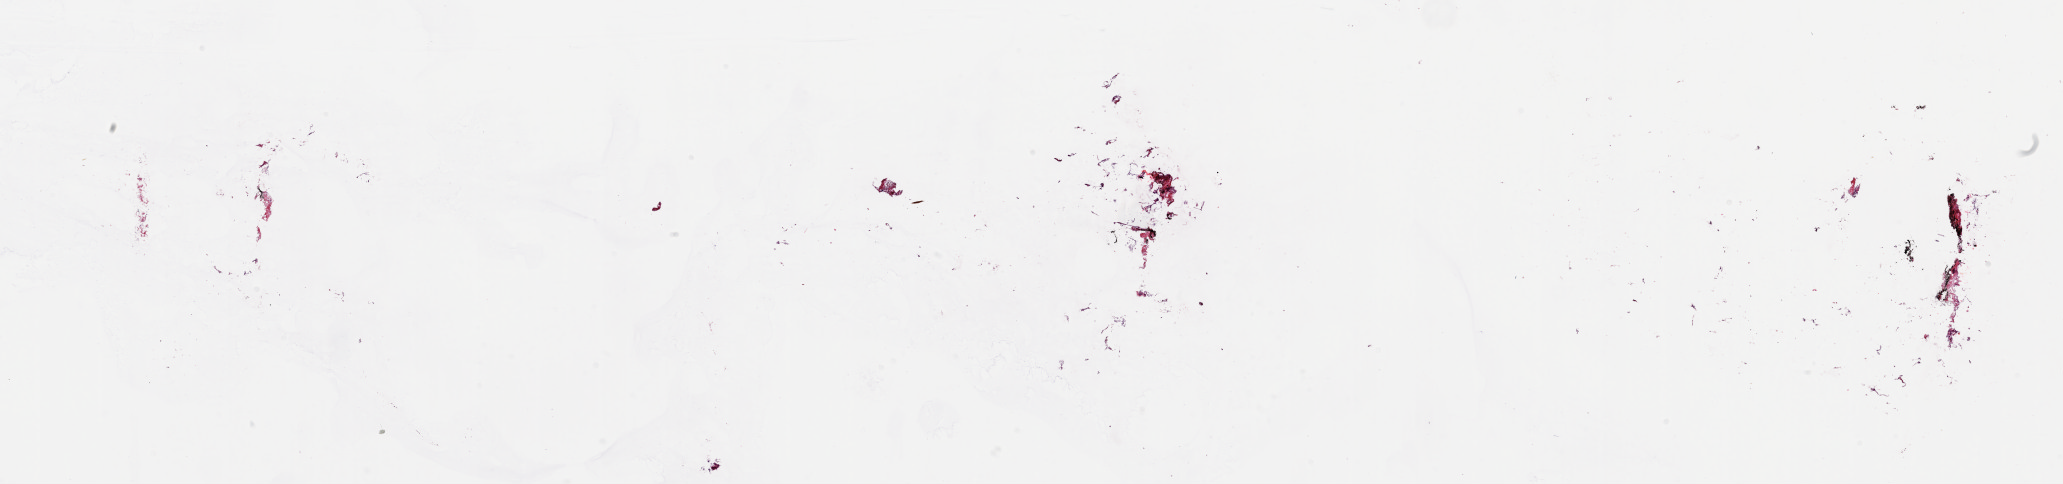
Digitized Hematoxylin and eosin (H&E) stained tissue section (whole slide) — shown as a low-resolution overview of the whole scanned area (about 32.7 x 7.7 mm, slide scanned at 20x). Frozen section from the top of the tissue portion. Solid tissue normal (non-tumour tissue) sample from the breast. Patient: female, age at initial diagnosis 54 years. Composition of this section per pathologist review: tumour cells 0%, tumour nuclei 0%, normal cells 0%, stromal cells 100%, necrosis 0%. Inflammatory infiltration, as recorded: lymphocyte infiltration 0%, monocyte infiltration 0%, neutrophil infiltration 0%.
This section: solid tissue normal sample (biorepository sample class). Patient diagnosis: Infiltrating duct carcinoma, NOS.